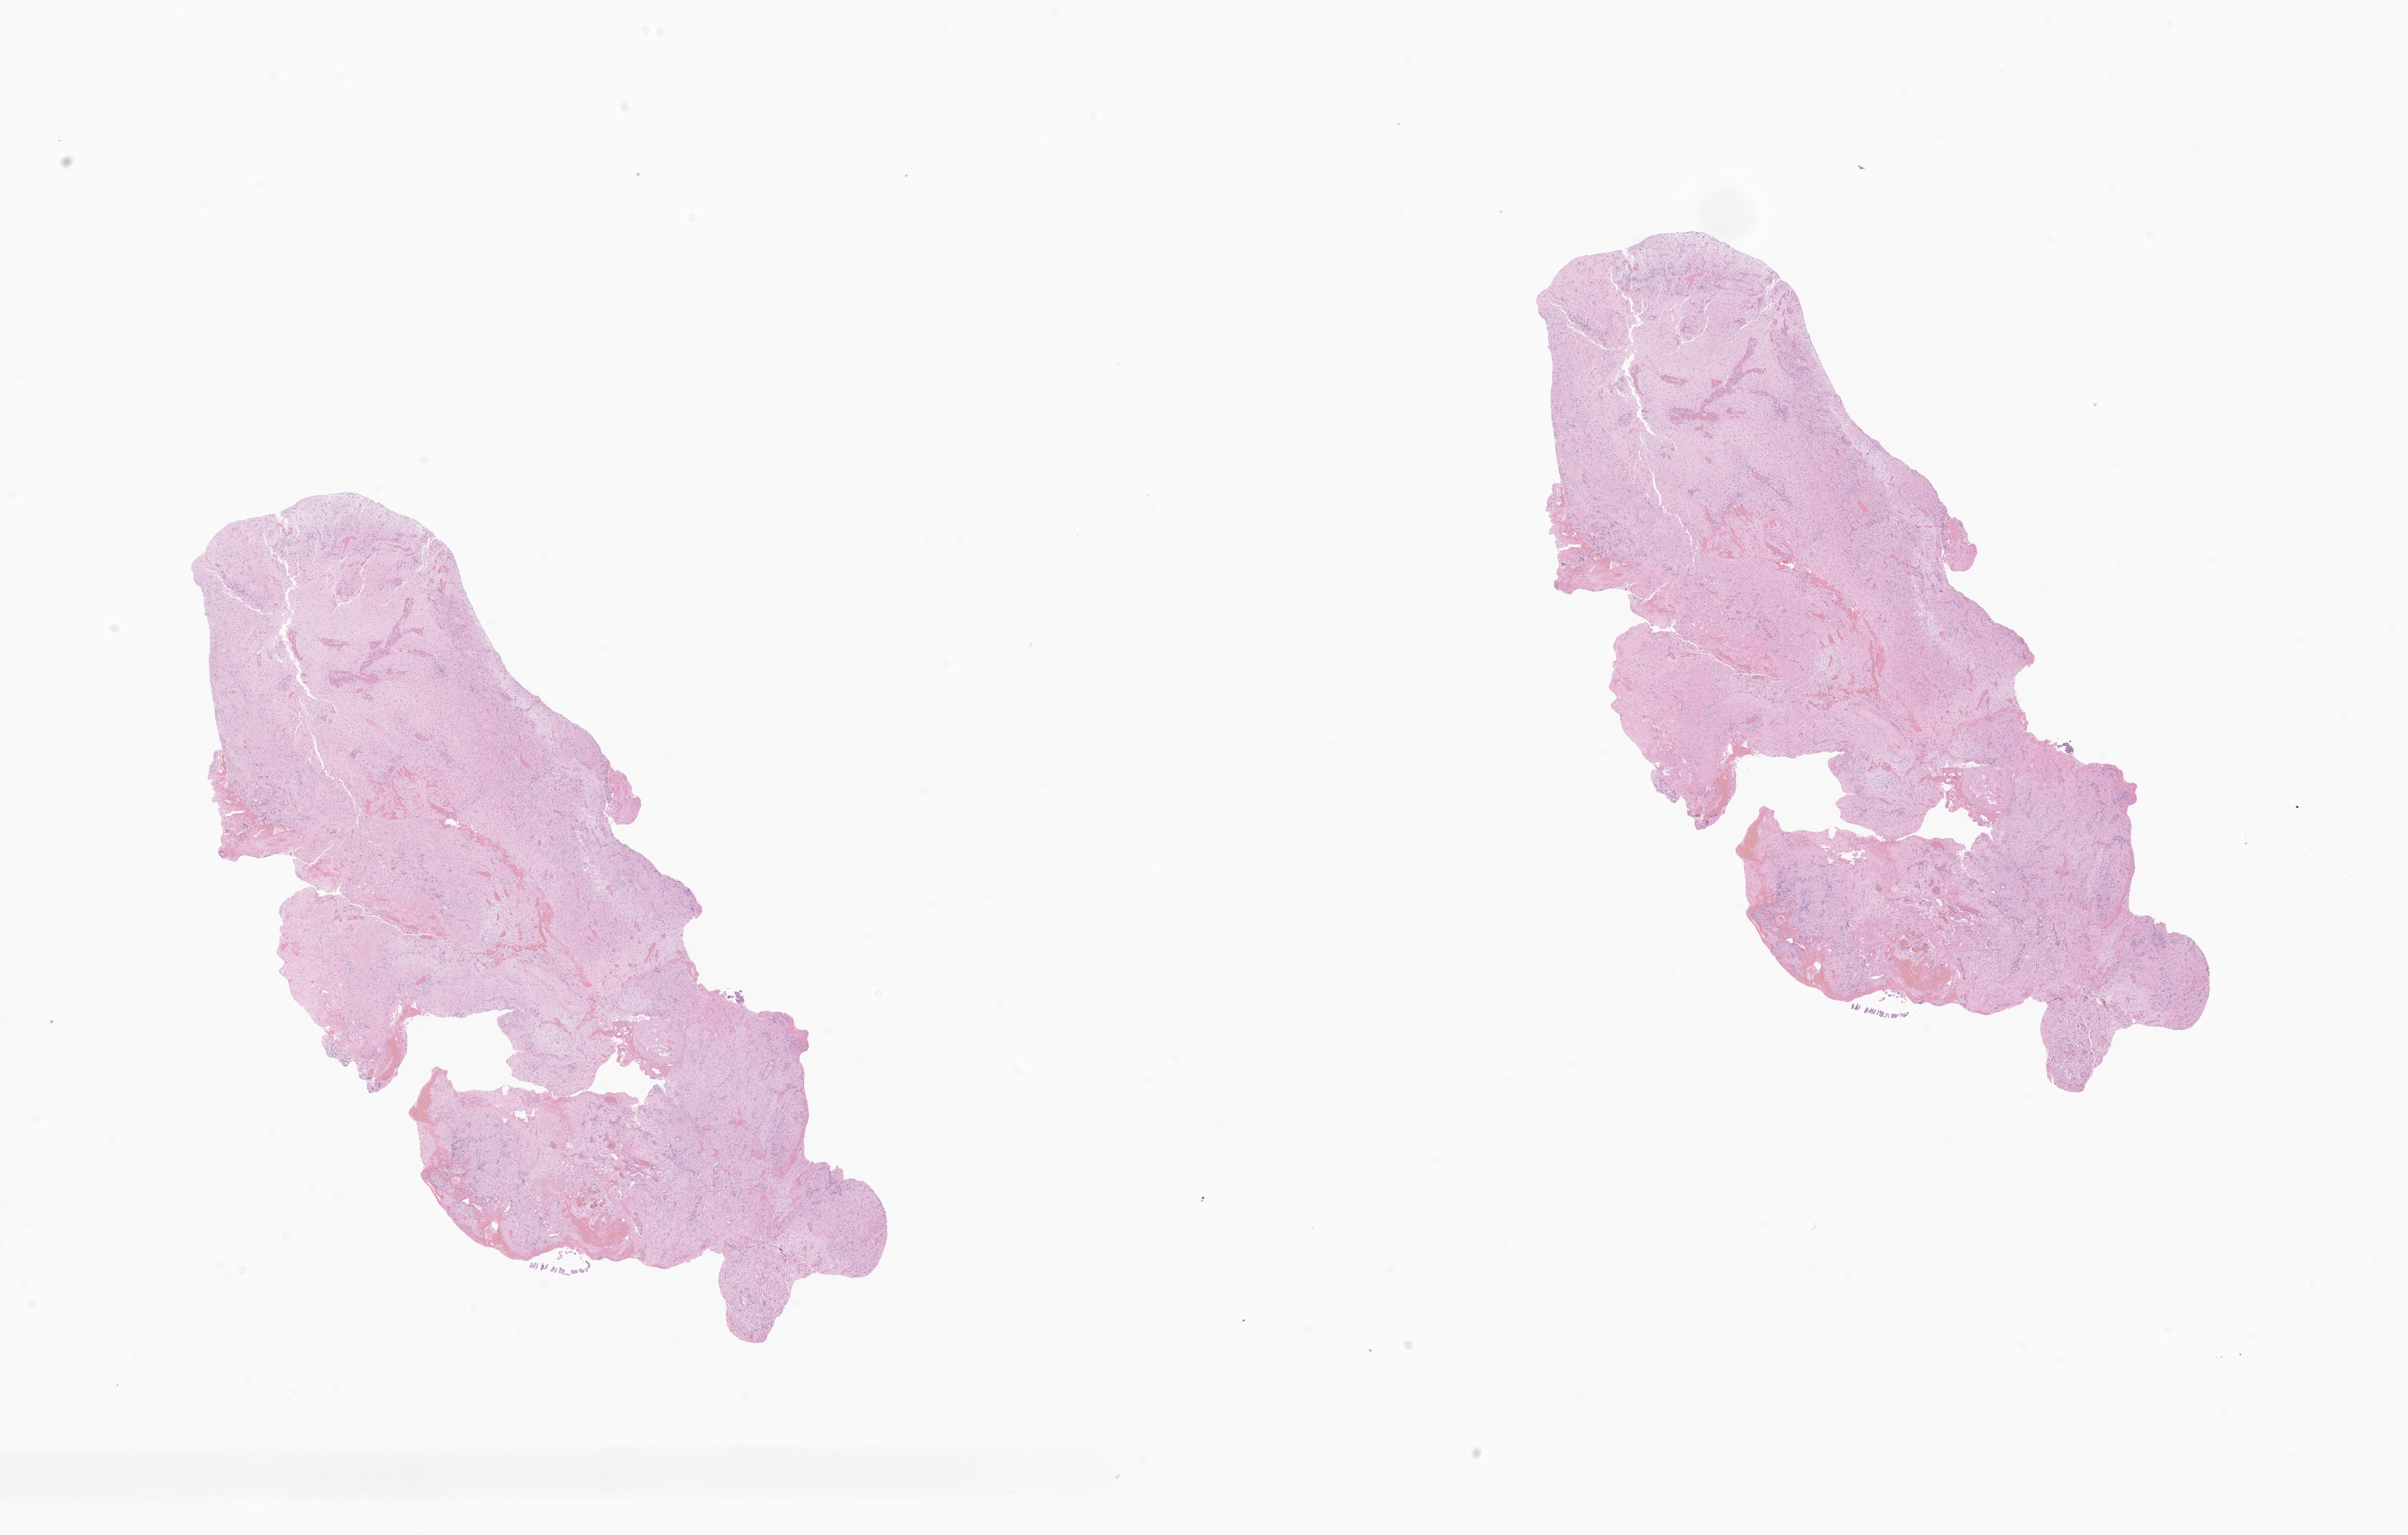
Whole-slide image, hematoxylin and eosin (H&E) stain of tumor tissue from the brain — low-resolution overview of the scanned area, about 22.6 x 14.4 mm, formalin-fixed, paraffin-embedded (FFPE) tissue. Female patient, age 93 months (7 years 9 months).
Recorded diagnosis: Pilocytic astrocytoma.